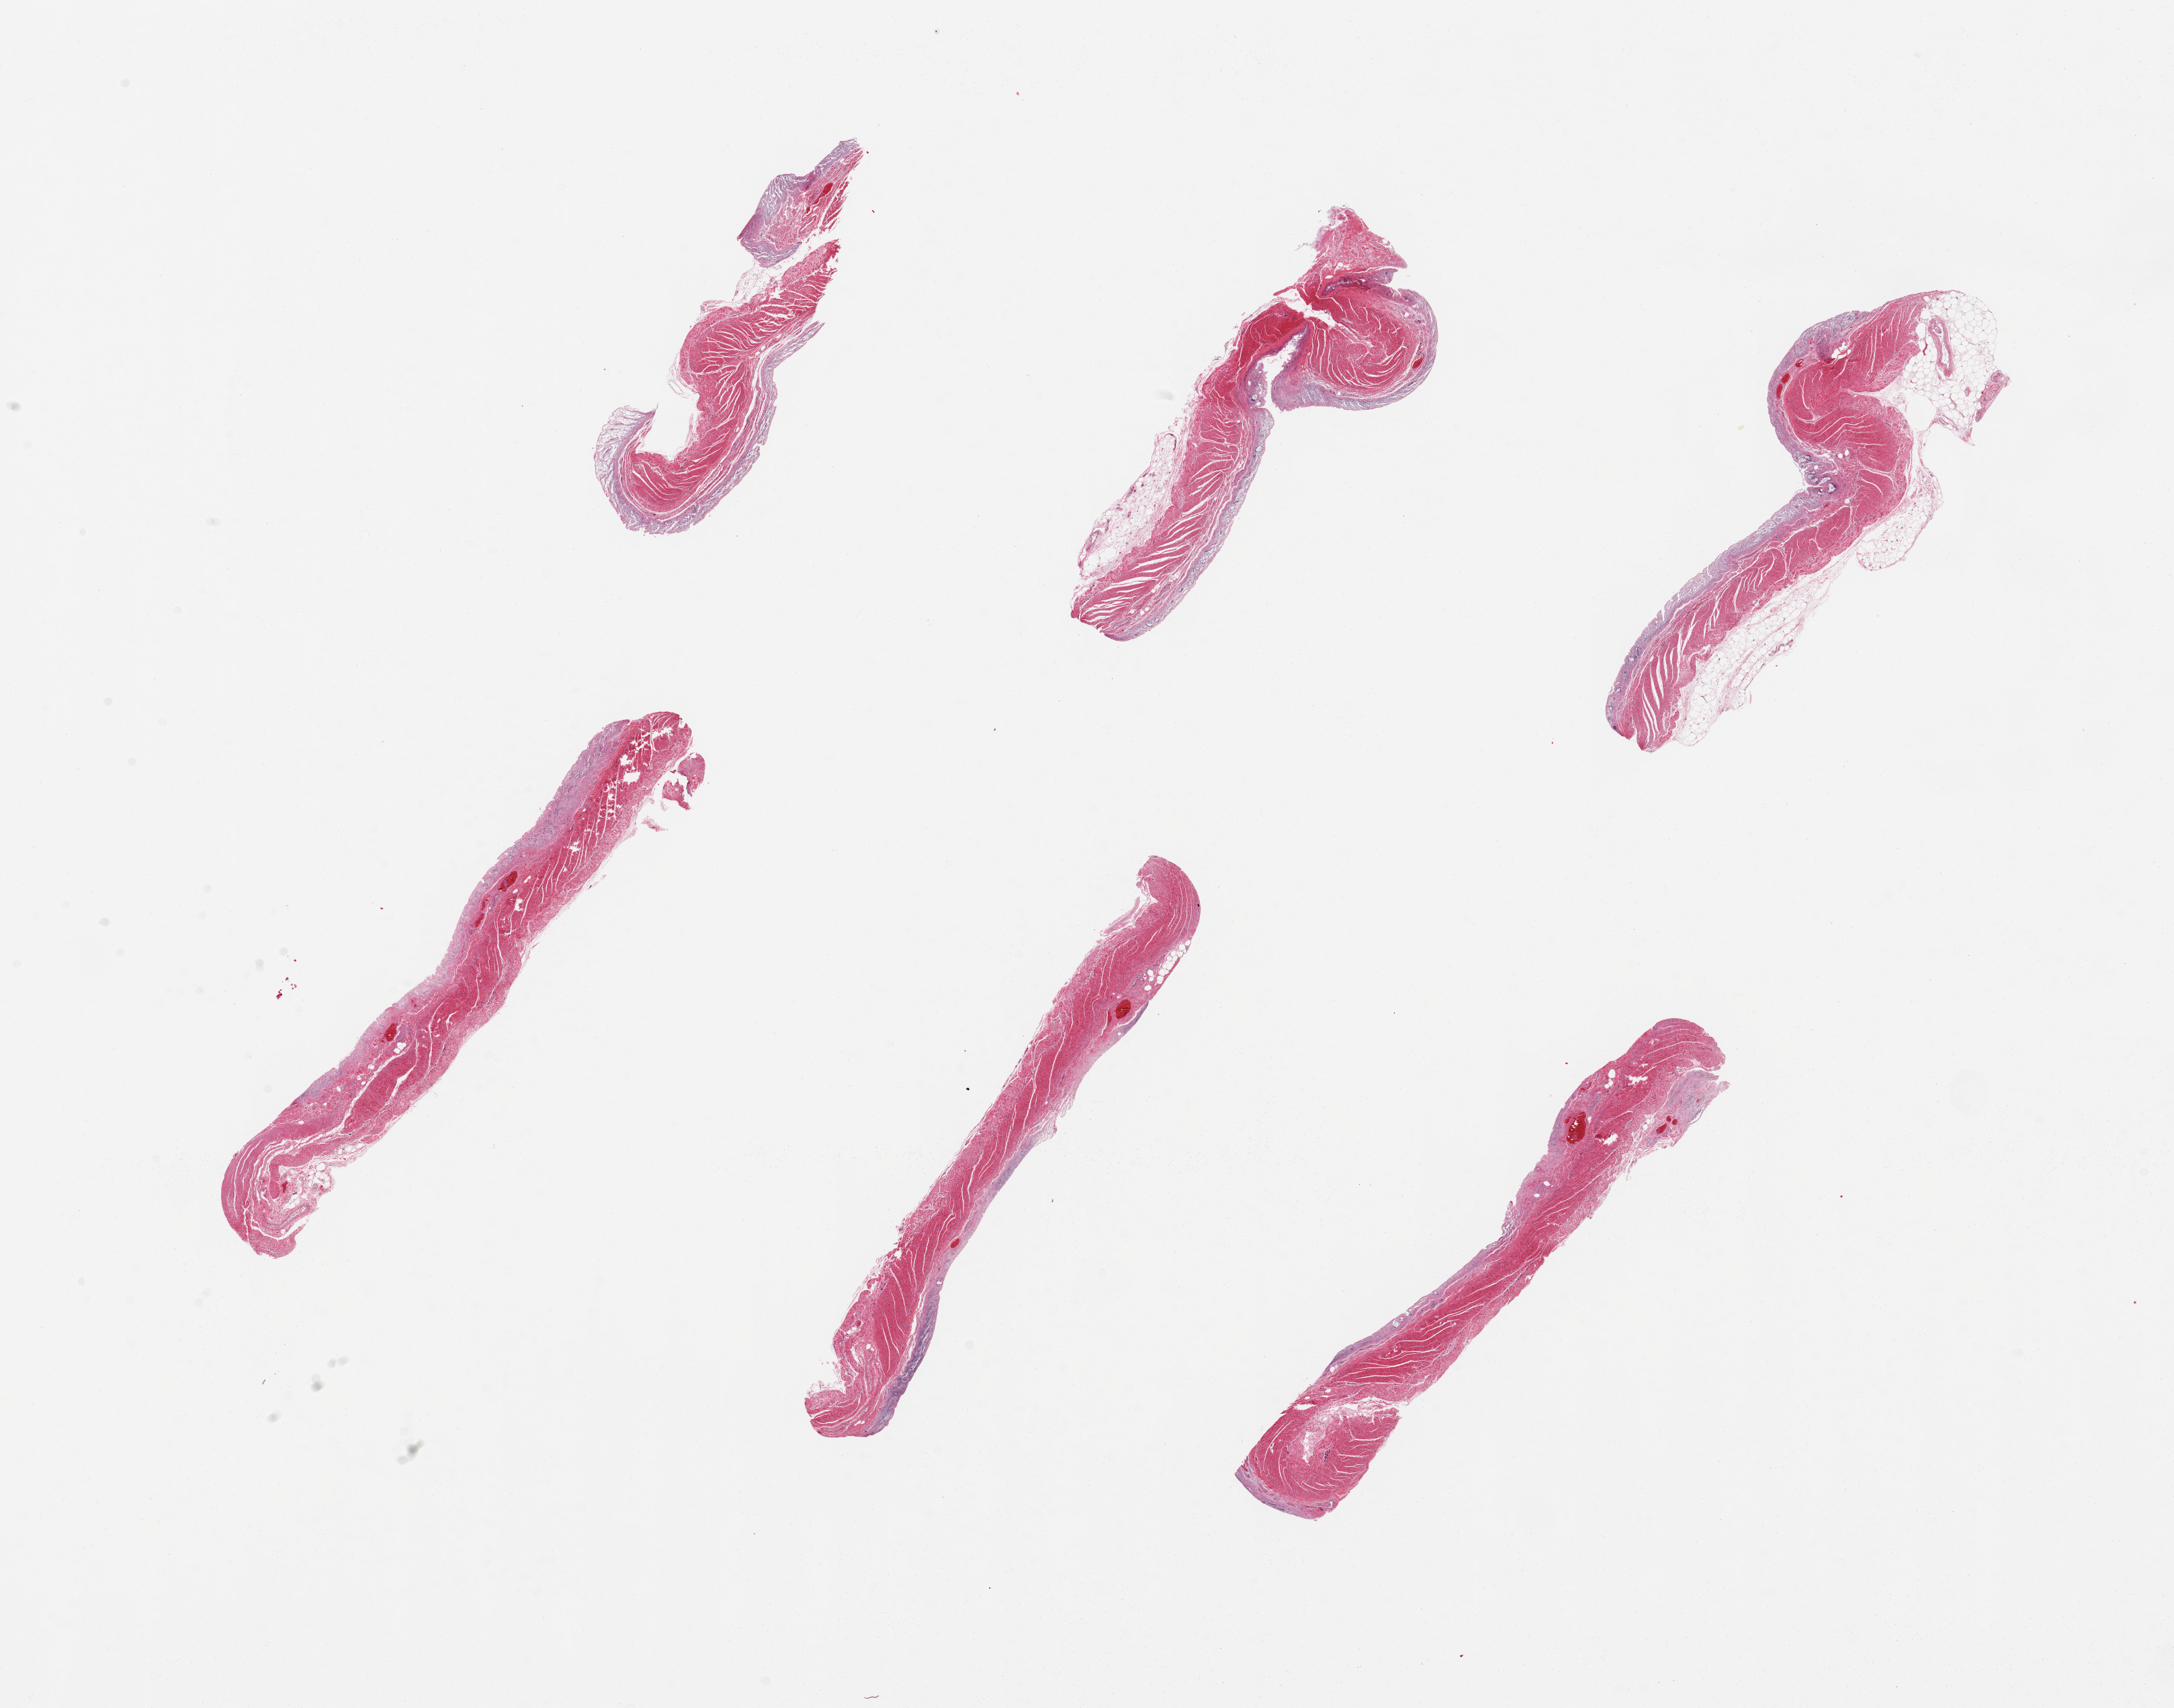
Digitized haematoxylin and eosin-stained section, brightfield — low-resolution overview of the scanned area, about 25.6 x 20.1 mm. PAXgene-fixed paraffin-embedded (PFPE) section. Target tissue: transverse colon. Tissue donor sample. Donor: male.
Pathologist's review note for this sample: 6 pieces, mucosa totally autolyzed.